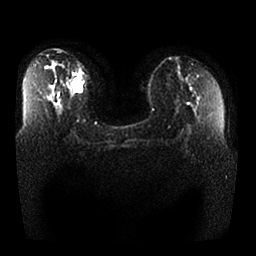
Breast MRI, one axial slice. Position 14 of 25 along the scan axis. Diffusion-weighted series; image 2 of 4 stored at this slice position (different b-values; order by instance number). 1.5 T. 4 mm slice thickness. 256 × 256 image matrix, field of view 370 × 370 mm. Female patient.
Annotated regions visible in this slice (expert manual segmentation):
- tumour on diffusion-weighted imaging: bounding box [x1, y1, x2, y2] px = [71, 78, 83, 93]